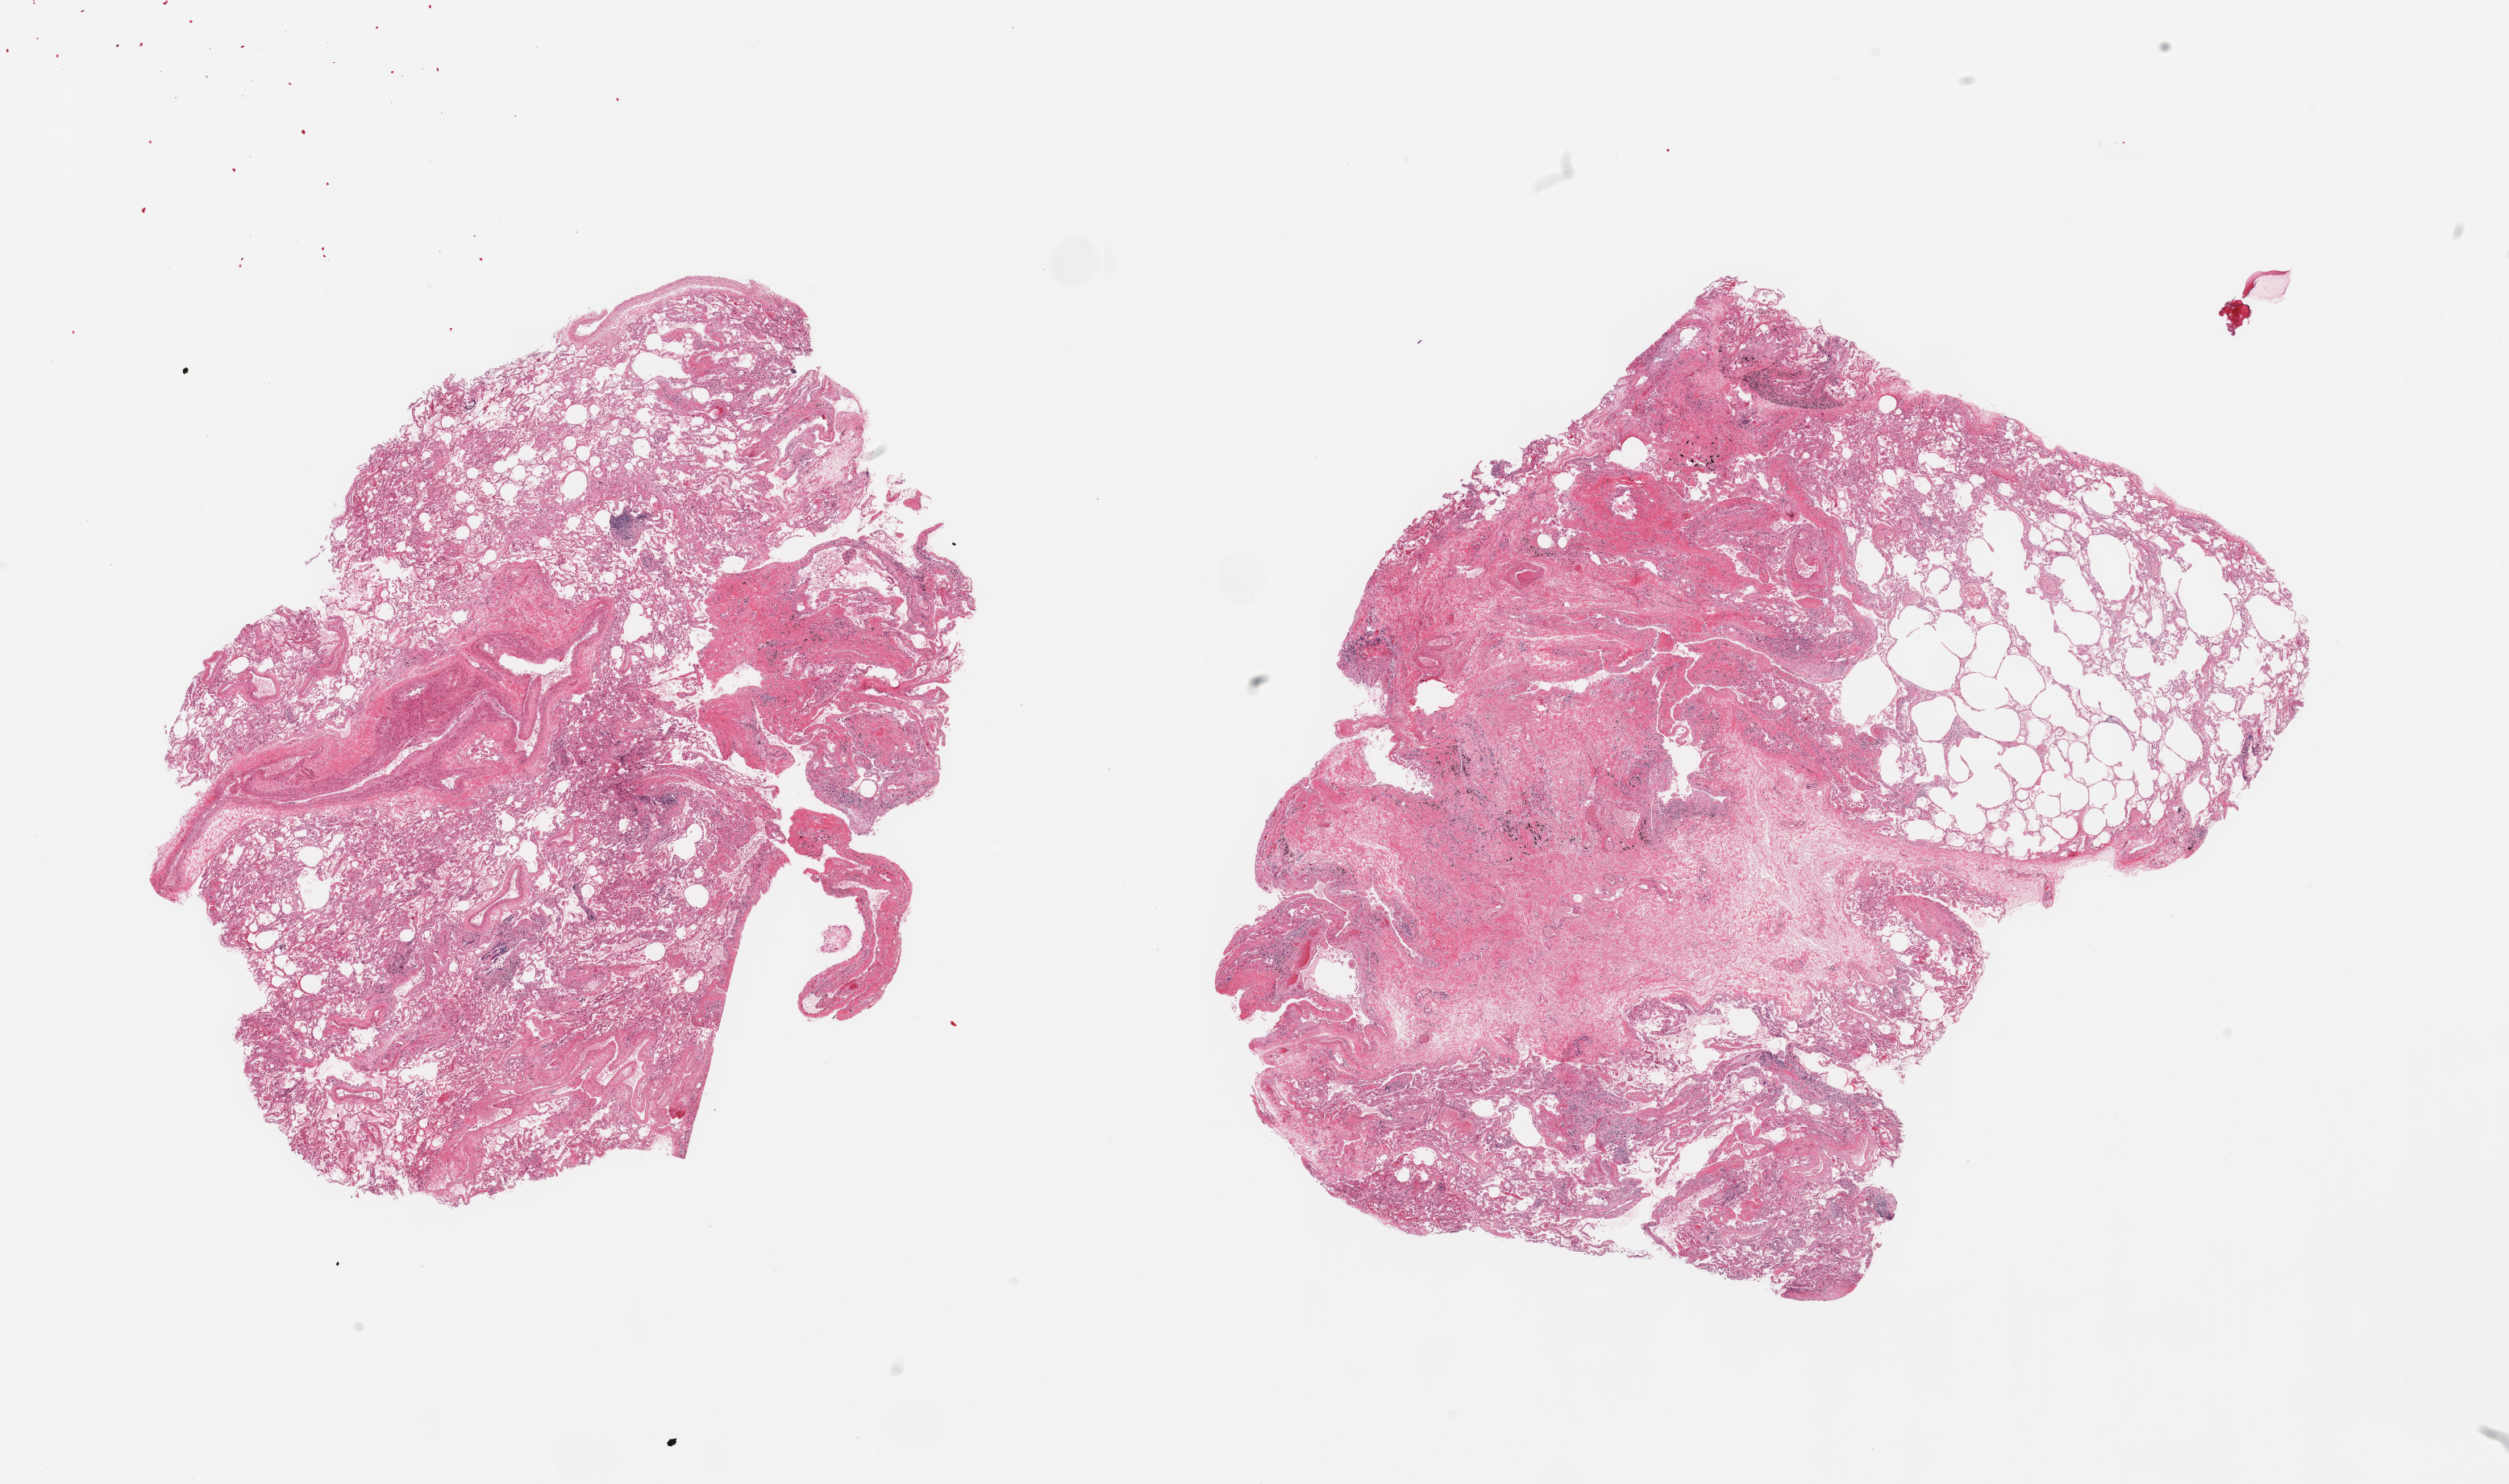
Haematoxylin and eosin whole-slide image — whole scanned area (about 24.6 x 14.6 mm, acquisition: 20x scan) shown as a low-resolution overview. PAXgene-fixed paraffin-embedded (PFPE) section. Section of lung (target tissue). Tissue donor sample. Male donor.
Review note (as recorded): 2 pieces, advanced fibrosing chronic pneumonitis, involves ~30% of tissue.